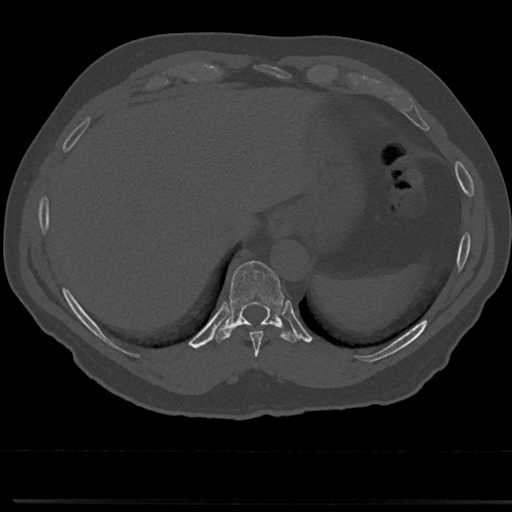
CT including the spine, one axial slice; slice 273 of 817 in the series (ordered by position); reconstruction kernel Br40s/3; 120 kVp; bone window (W 1800 / L 400 HU); 512 × 512 image matrix, field of view 355 × 355 mm. Male patient, age 61 years. Case-level facts recorded for this patient, not image findings: primary cancer: prostate.
Structures marked on this image (semi-automatic segmentation, software-assisted and operator-edited):
- T10 vertebra: bounding box [x1, y1, x2, y2] px = [230, 261, 282, 323]
- T8 vertebra: [239, 318, 281, 322]
- T9 vertebra: [232, 297, 284, 350]